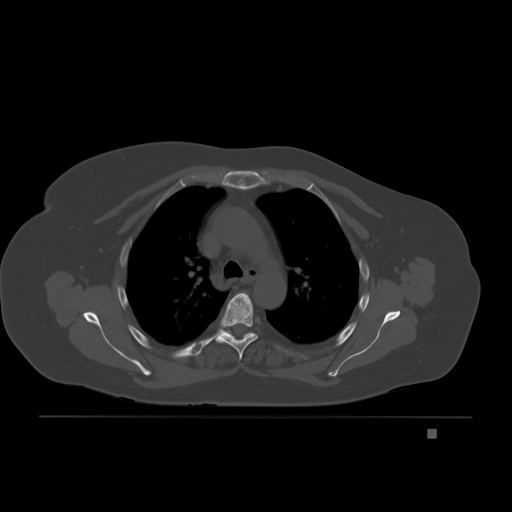
CT including the spine, one axial slice. Slice 151 of 221 in the series (ordered by position). Bone window (W 1800 / L 400 HU). 3 mm slice thickness. 512 × 512 image matrix, field of view 474 × 474 mm. Female patient, age 63 years. From the clinical record (not read from this slice): primary cancer: breast.
Outlined on this slice (semi-automatically segmented with operator editing):
- T4 vertebra: bounding box (x1, y1, x2, y2) in pixels: (216, 293, 257, 359)
- T5 vertebra: (226, 331, 231, 334)